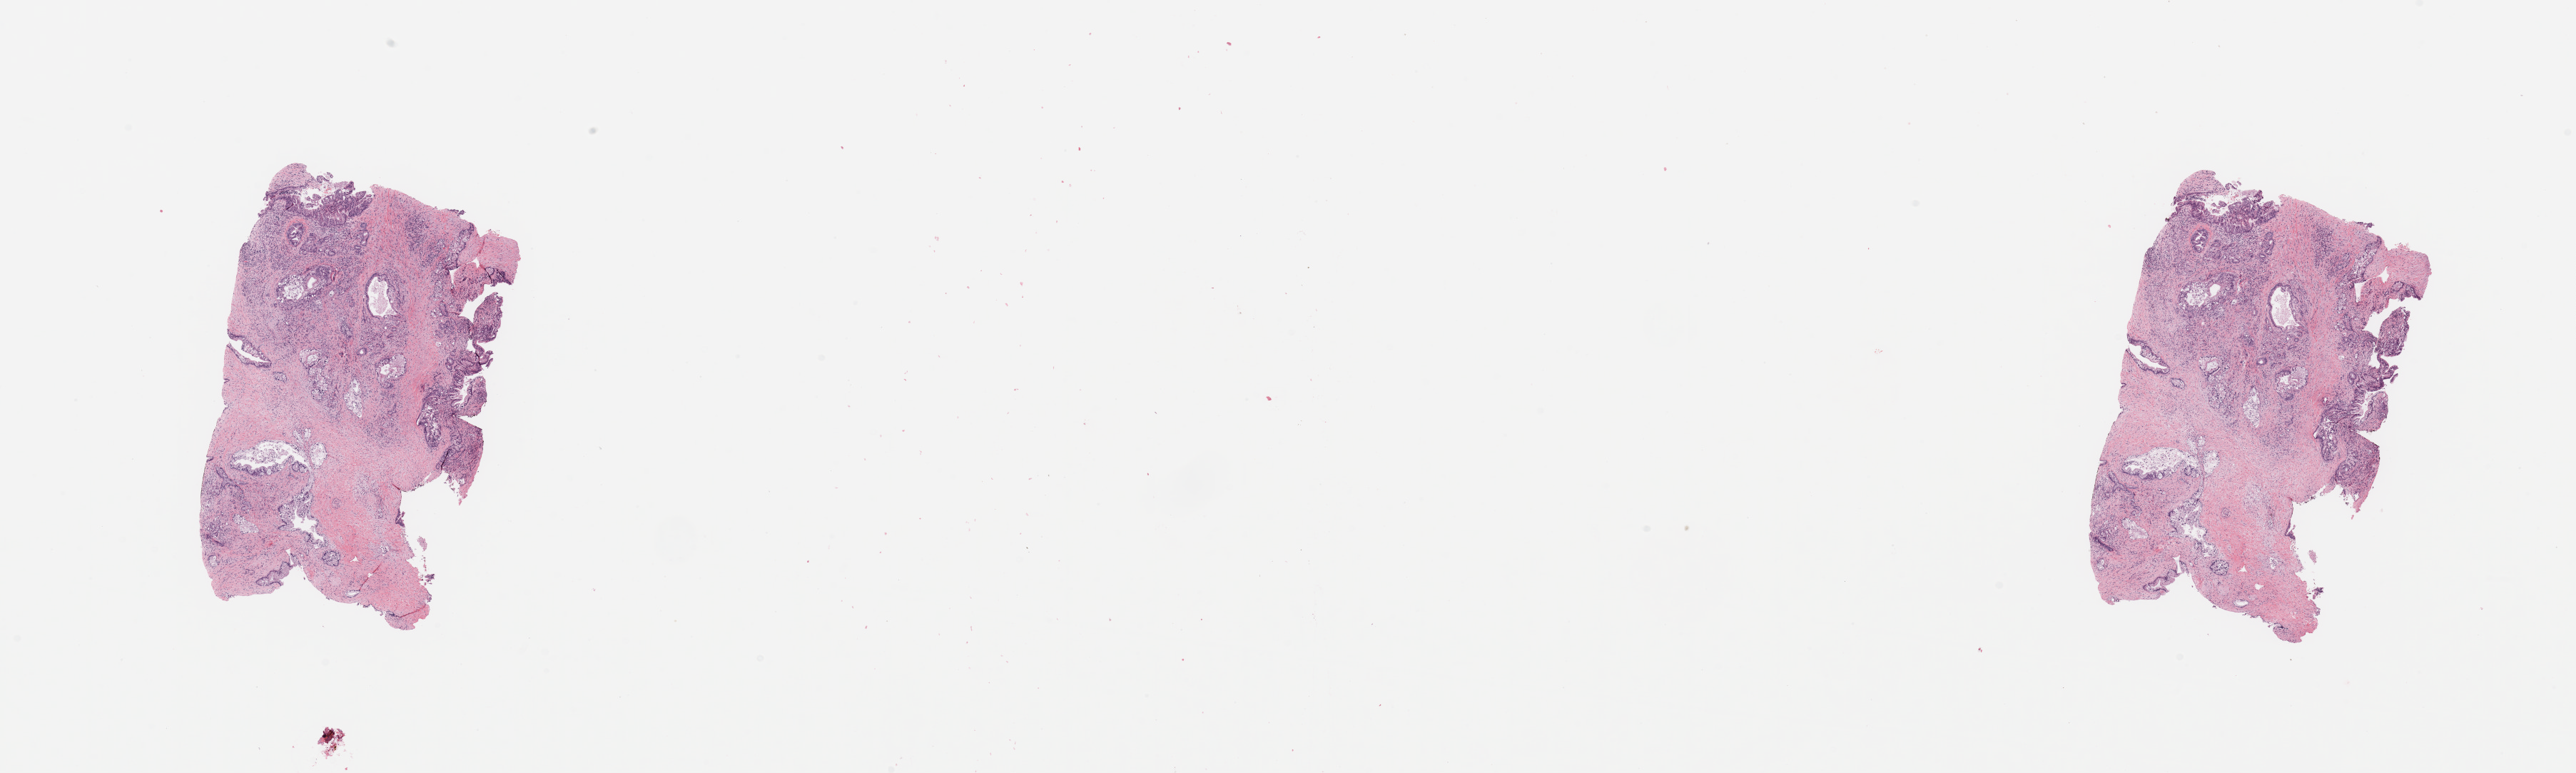
H&E-stained whole-slide image — low-resolution overview of the scanned area, about 28.5 x 8.6 mm. Tumour tissue sample, sampled site: pancreas. Patient: male, age 67 years. Histologic grade: G2 (moderately differentiated). Pathologist review of this section (percent, as recorded): tumour nuclei 25%, necrosis 0%.
Diagnosis: Infiltrating duct carcinoma, NOS. AJCC pathologic stage: IB.